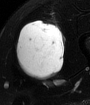
MRI of an extremity soft-tissue mass, one axial slice; position 33 of 65 along the scan axis; T2-weighted fat-saturated; MR volume resampled by the dataset authors to the PET/CT grid (not the native acquisition matrix); 3.27 mm slice thickness; 90 × 105 image matrix, field of view 88 × 103 mm. Male patient. From the clinical record (not read from this slice): histological type: mixoid liposarcoma; grade: low; site of the primary tumour: left thigh.
Outlined on this slice (expert contour drawn on MRI and transferred to this co-registered scan by the dataset authors):
- gross tumour volume (mass): box from (x=16, y=21) to (x=65, y=79) px